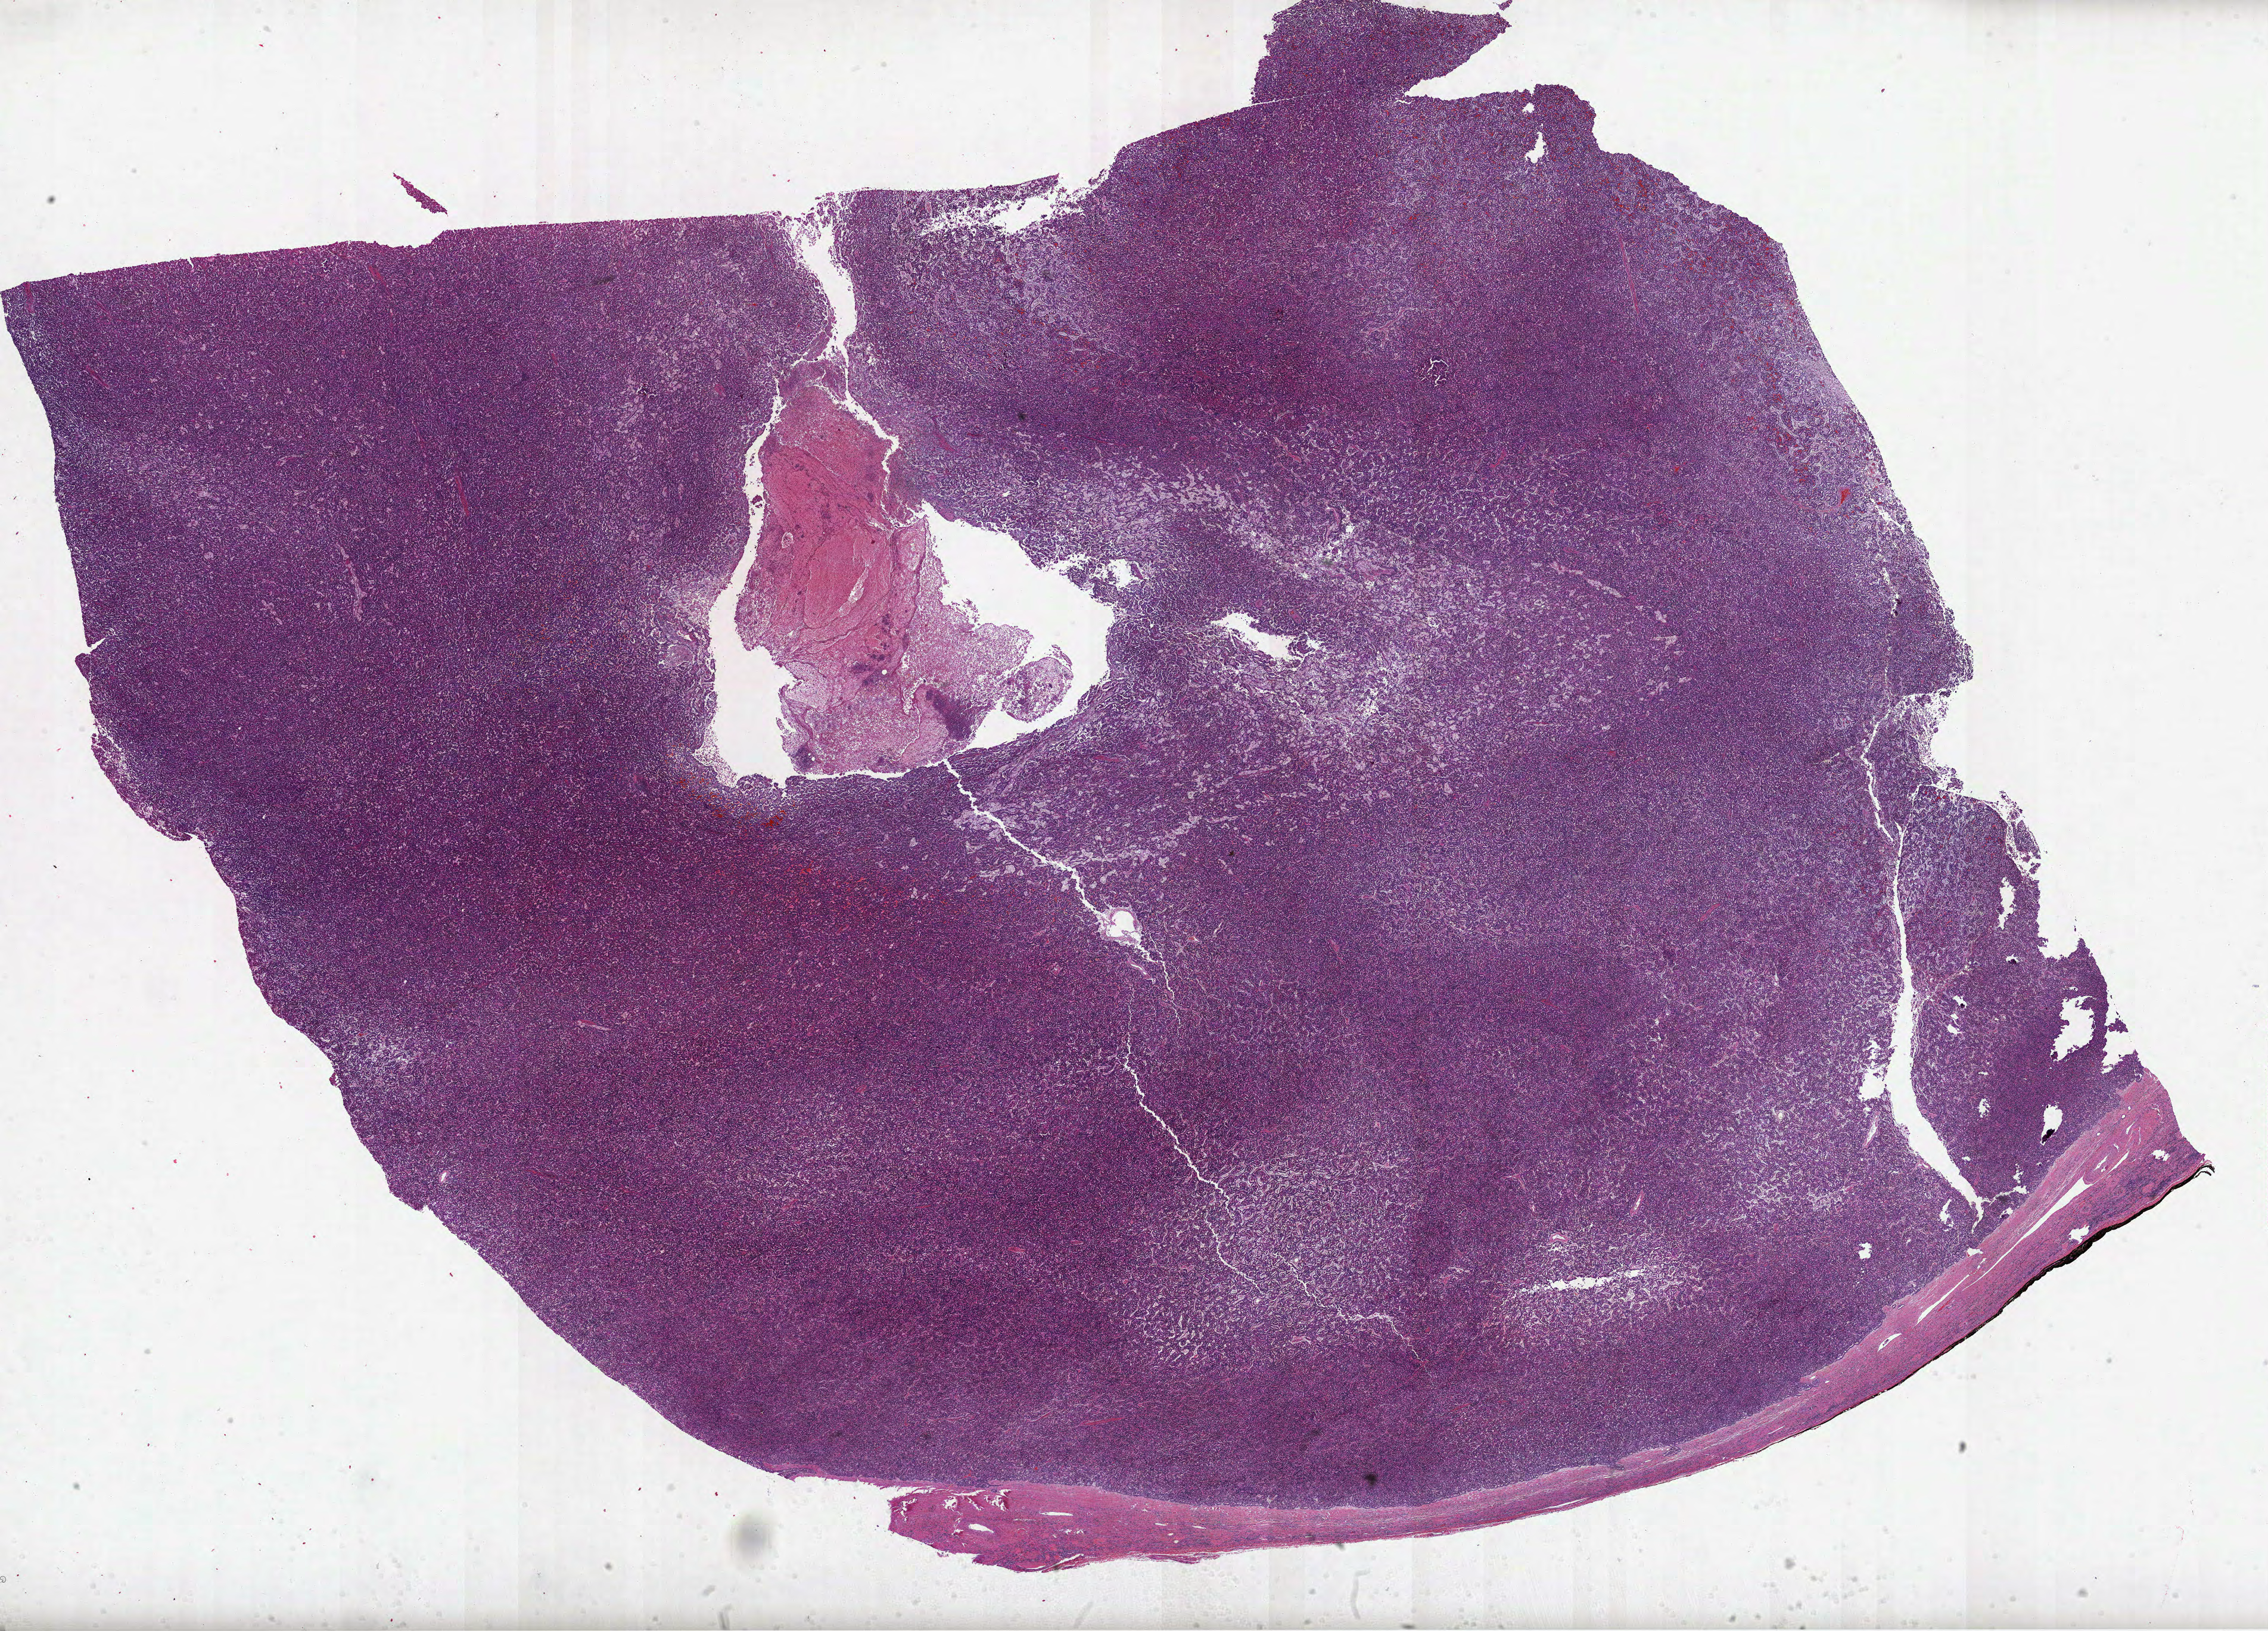
Digitized H&E-stained tissue section (whole slide) — low-resolution overview of the scanned area, about 30.7 x 22.1 mm (from a 40x scan). Formalin-fixed paraffin-embedded (FFPE) diagnostic section. Primary tumour sample from the kidney. Female, age 38 years at initial diagnosis.
Diagnosis: Papillary adenocarcinoma, NOS. AJCC pathologic stage: I.